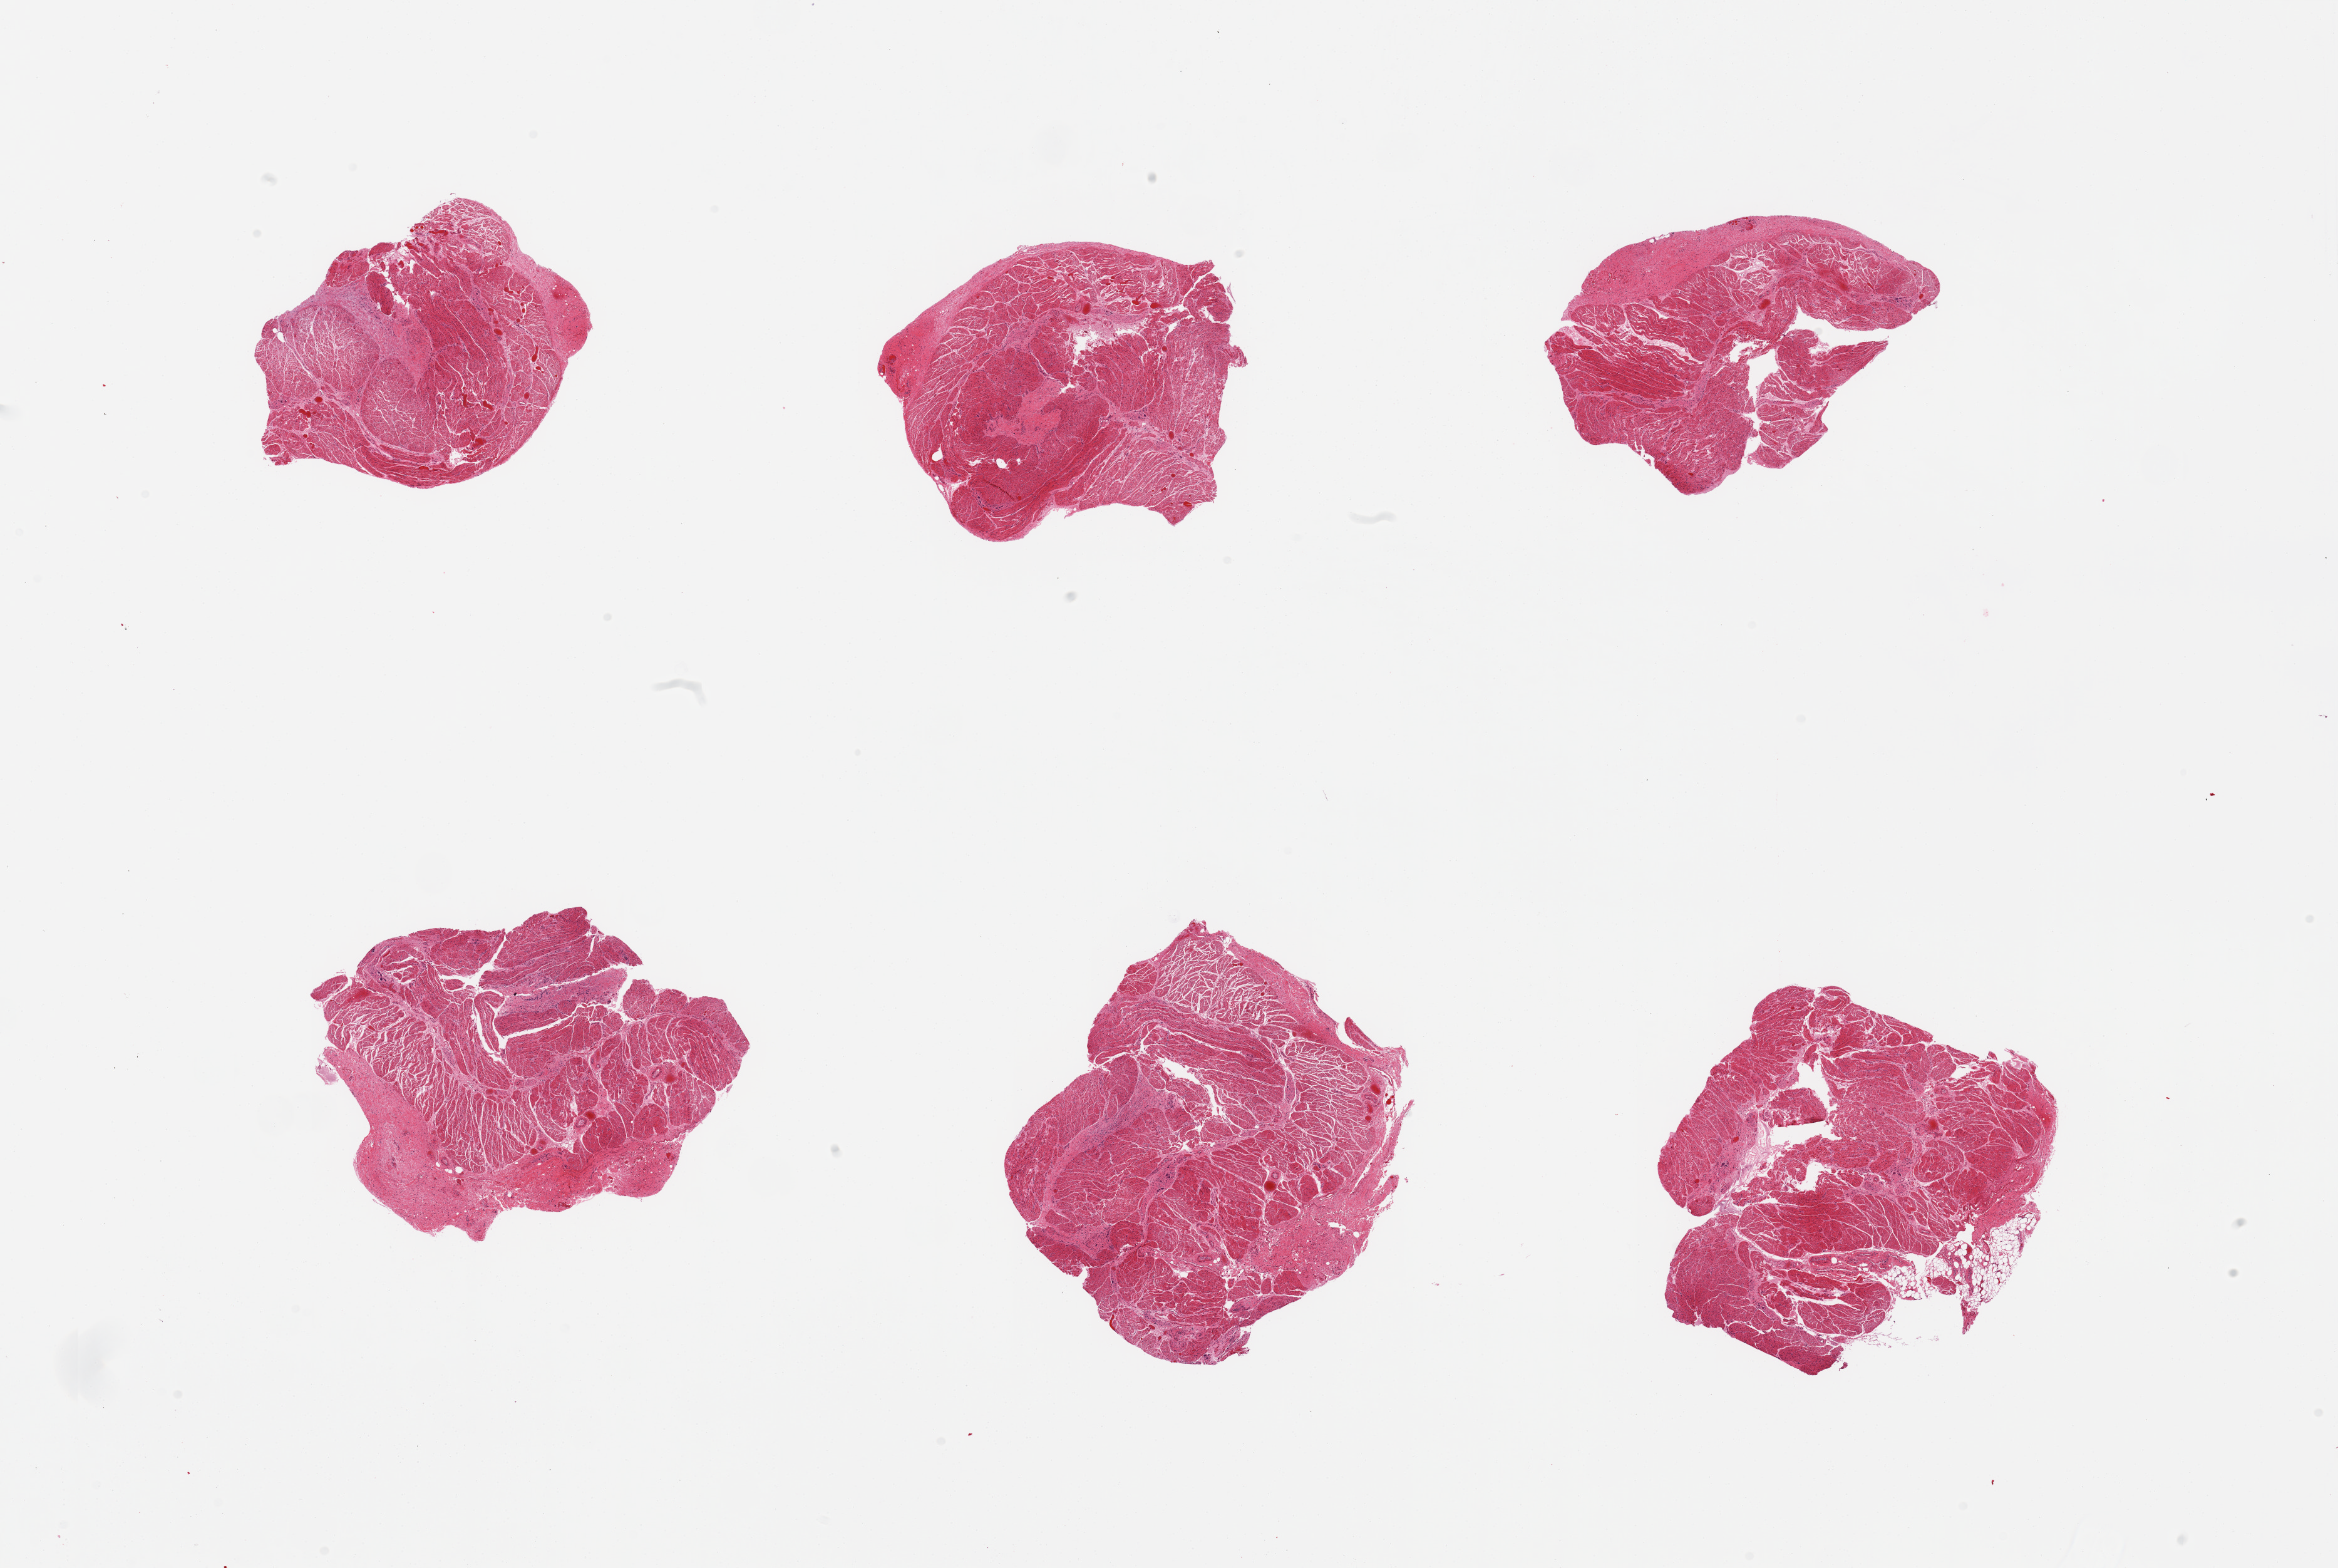
Whole-slide image, haematoxylin and eosin stain — shown as a low-resolution overview of the whole scanned area (about 29.5 x 19.8 mm); PAXgene-fixed paraffin-embedded (PFPE) section; section of gastroesophageal junction (target tissue); donor tissue sample. Male donor.
Reviewer comment on this tissue sample: 6 pieces, all muscularis, good specimens.